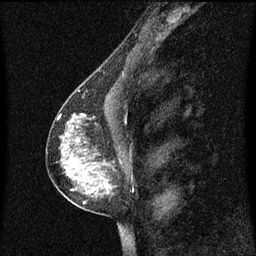
Breast MRI (dynamic contrast-enhanced), one sagittal slice; slice 37 of 60 in the series (ordered by position); dynamic contrast-enhanced series, image 2 of 3 at this slice position (ordered by acquisition); 1.5 T; TE 4.2 ms, TR 8.4 ms; 2 mm slice thickness; 256 × 256 image matrix, field of view 200 × 200 mm. Female patient, age 40 years. Case-level facts recorded for this patient, not image findings: setting: breast cancer imaged before/during neoadjuvant chemotherapy; receptor status: triple-negative.
Annotated regions visible in this slice (semi-automatically segmented with operator editing):
- analysis volume of interest (the breast-tissue region the enhancement analysis was run in; not a lesion): bounding box [x1, y1, x2, y2] px = [60, 104, 125, 211]
- tumour enhancement mask (voxels above the 70 % enhancement threshold inside the analysis volume of interest): [76, 140, 111, 193]